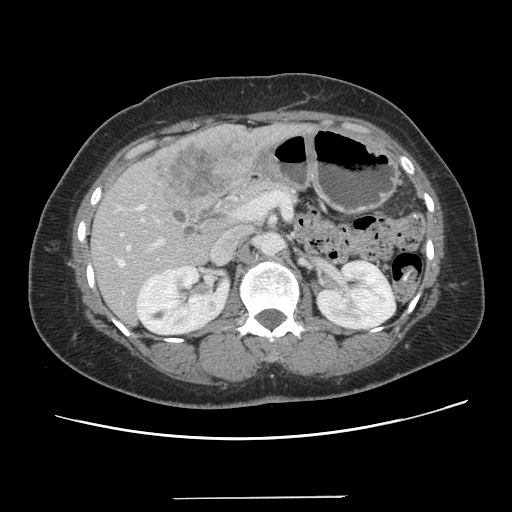
Contrast-enhanced abdominal CT, one axial slice; slice 64 of 141 in the series (ordered by position); intravenous contrast given; soft-tissue window (W 400 / L 40 HU); 512 × 512 image matrix, field of view 366 × 366 mm. Female patient, age 53 years. Case-level facts recorded for this patient, not image findings: diagnosis: colorectal cancer liver metastases, imaged before liver resection; multiple liver metastases: no; largest metastasis: 14.5 cm; disease in both lobes: yes.
Structures marked on this image (outlined manually by an expert reader):
- hepatic veins: bounding box [x1, y1, x2, y2] px = [118, 245, 129, 265]
- liver: [91, 125, 301, 323]
- planned liver remnant (the part of the liver to remain after resection): [91, 212, 217, 325]
- portal vein (with intrahepatic branches): [121, 205, 162, 248]
- liver metastasis: [153, 139, 248, 198]